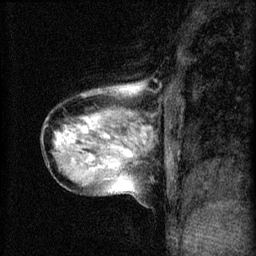
Breast MRI (dynamic contrast-enhanced), one sagittal slice. Position 22 of 60 along the scan axis. 3 images stored at this slice position (order not interpretable as contrast timing). 1.5 T. TE 4.2 ms, TR 8.2 ms. 256 × 256 image matrix, field of view 180 × 180 mm. Female patient, age 40 years.
Annotated regions visible in this slice (semi-automatically segmented with operator editing):
- analysis volume of interest (the breast-tissue region the enhancement analysis was run in; not a lesion): bounding box [x1, y1, x2, y2] px = [40, 80, 165, 205]
- tumour enhancement mask (voxels above the 70 % enhancement threshold inside the analysis volume of interest): [57, 118, 147, 169]